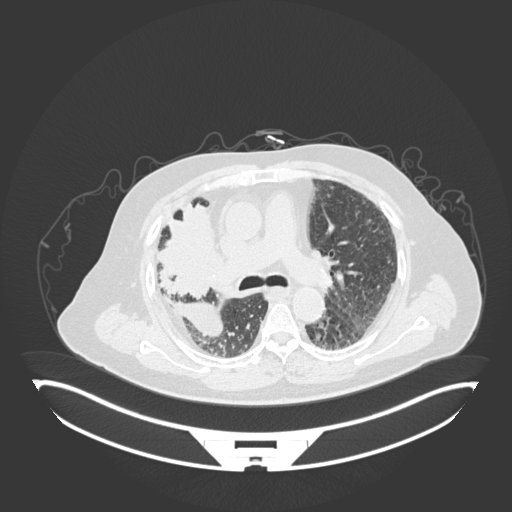
Chest CT, one axial slice. Slice 106 of 201 in the series (ordered by position). 120 kVp. Lung window (W 1500 / L -600 HU). 1 mm slice thickness. 512 × 512 image matrix, field of view 500 × 500 mm. Male patient, age 69 years. Case-level facts recorded for this patient, not image findings: clinical TNM (as recorded): T4 N3 M1.
Annotated regions visible in this slice (bounding box drawn by a radiologist):
- lung tumour (recorded histology: adenocarcinoma): bounding box (x1, y1, x2, y2) in pixels: (158, 200, 233, 302)